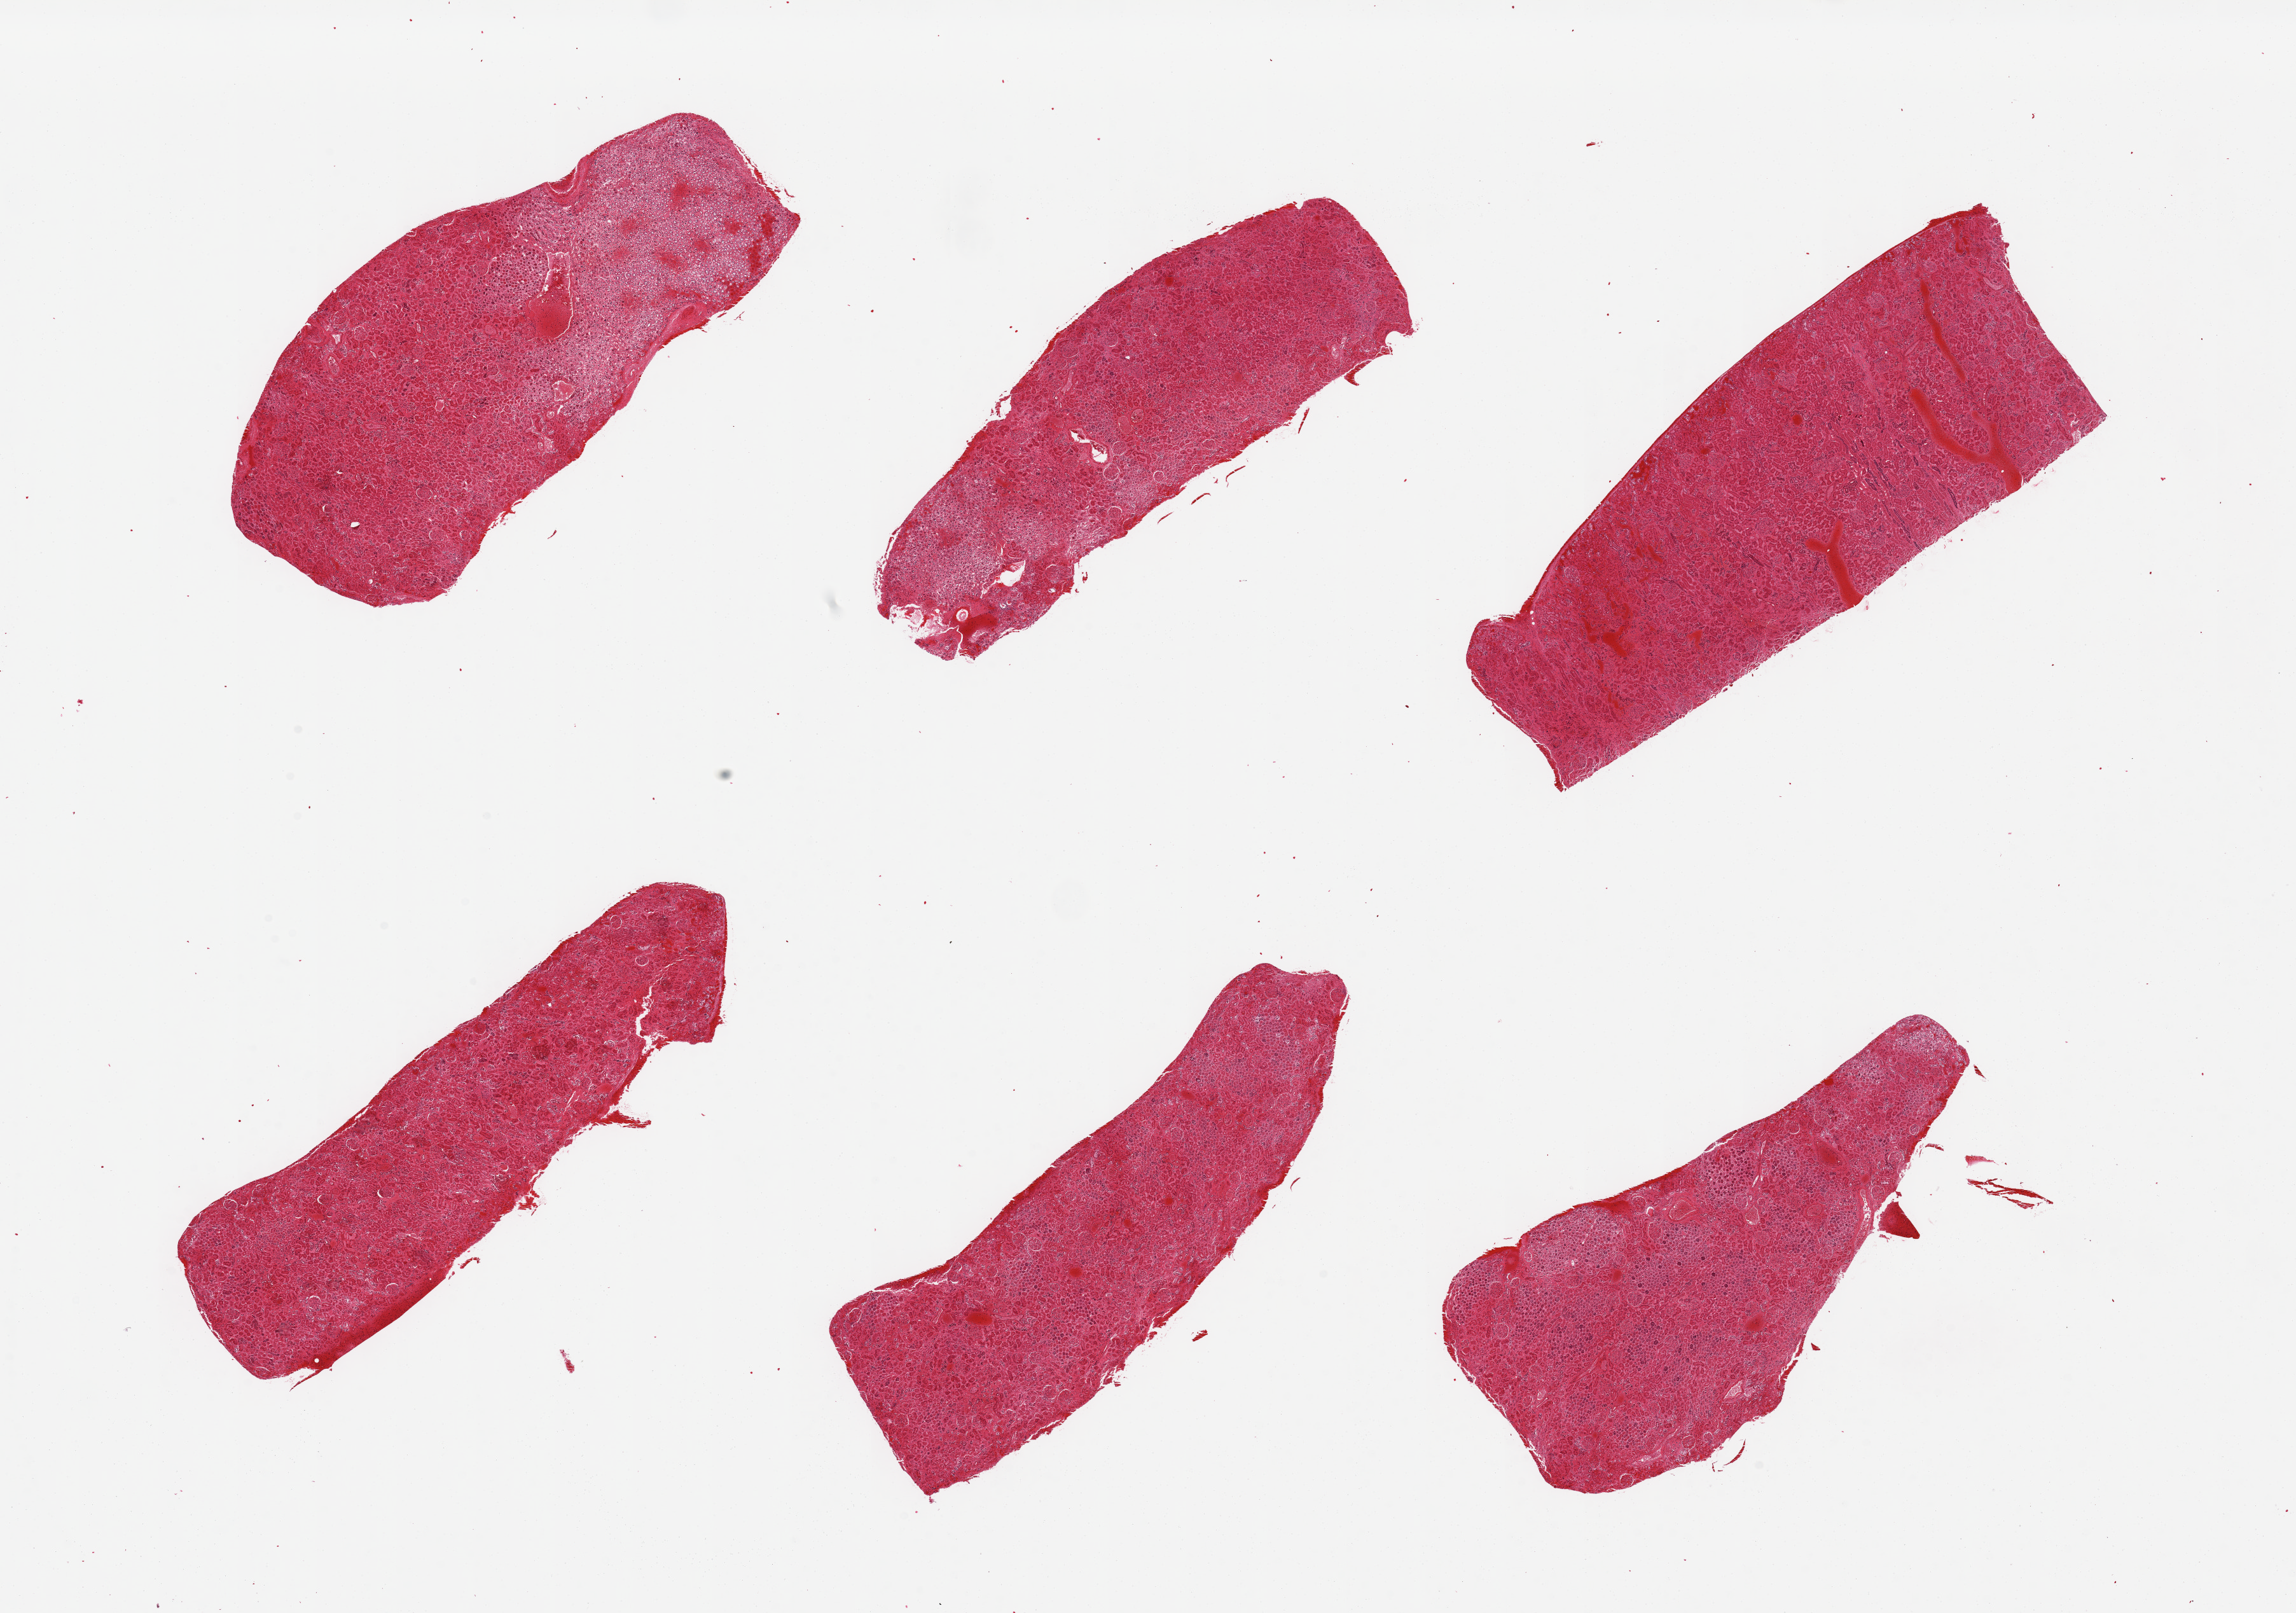
Digitized H&E-stained section, brightfield, a low-resolution overview of the entire scanned area, about 28.5 x 20.1 mm. PAXgene-fixed, paraffin-embedded tissue. Section of renal cortex (target tissue). Donor tissue sample. Donor: male.
Pathologist's review note for this sample: 6 pieces; acute vascular congestion.